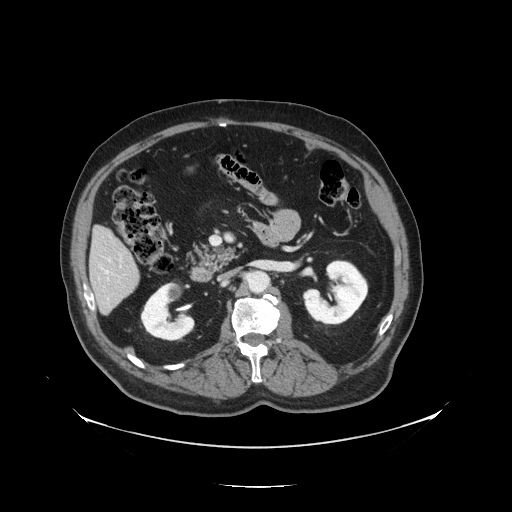
Contrast-enhanced abdominal CT, one axial slice; position 55 of 138 along the scan axis; soft-tissue window (W 400 / L 40 HU); 512 × 512 image matrix, field of view 497 × 497 mm. Male patient, age 77 years. From the clinical record (not read from this slice): diagnosis: colorectal cancer liver metastases, imaged before liver resection; multiple liver metastases: no; largest metastasis: 1.5 cm; disease in both lobes: no.
Structures marked on this image (outlined manually by an expert reader):
- liver: bounding box (x1, y1, x2, y2) in pixels: (91, 229, 140, 312)
- planned liver remnant (the part of the liver to remain after resection): (92, 229, 137, 283)